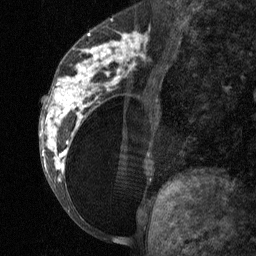
Breast MRI (dynamic contrast-enhanced), one sagittal slice. Position 29 of 64 along the scan axis. Dynamic contrast-enhanced study with each time point stored as its own series, time point 2 of 3 at this slice position (early post-contrast, ordered by acquisition time). 1.5 T. TE 4.8 ms, TR 27 ms. 2 mm slice thickness. 256 × 256 image matrix, field of view 180 × 180 mm. Patient: female, 34 years. From the clinical record (not read from this slice): setting: breast cancer imaged before/during neoadjuvant chemotherapy; receptor status: HR-positive, HER2-negative.
Annotated regions visible in this slice (semi-automatic segmentation, software-assisted and operator-edited):
- analysis volume of interest (the breast-tissue region the enhancement analysis was run in; not a lesion): bounding box <41,23,157,197> (left, top, right, bottom; pixels)
- tumour enhancement mask (voxels above the 90 % enhancement threshold inside the analysis volume of interest): <41,31,142,181>